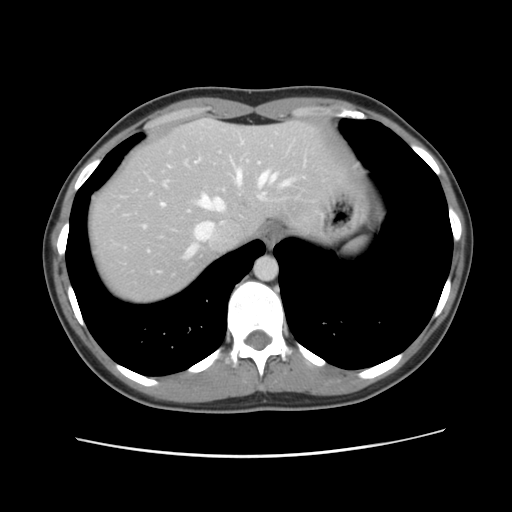
Contrast-enhanced abdominal CT, one axial slice. Slice 101 of 134 in the series (ordered by position). 120 kVp. Intravenous contrast given. Soft-tissue window (W 400 / L 40 HU). 2.5 mm slice thickness. 512 × 512 image matrix, field of view 339 × 339 mm. Female patient, age 33 years. From the clinical record (not read from this slice): diagnosis: colorectal cancer liver metastases, imaged before liver resection; multiple liver metastases: yes; largest metastasis: 4.5 cm.
Annotated regions visible in this slice (manually delineated by an expert):
- hepatic veins: box from (x=162, y=159) to (x=294, y=257) px
- liver: (x=87, y=120)–(x=344, y=304)
- planned liver remnant (the part of the liver to remain after resection): (x=88, y=120)–(x=344, y=304)